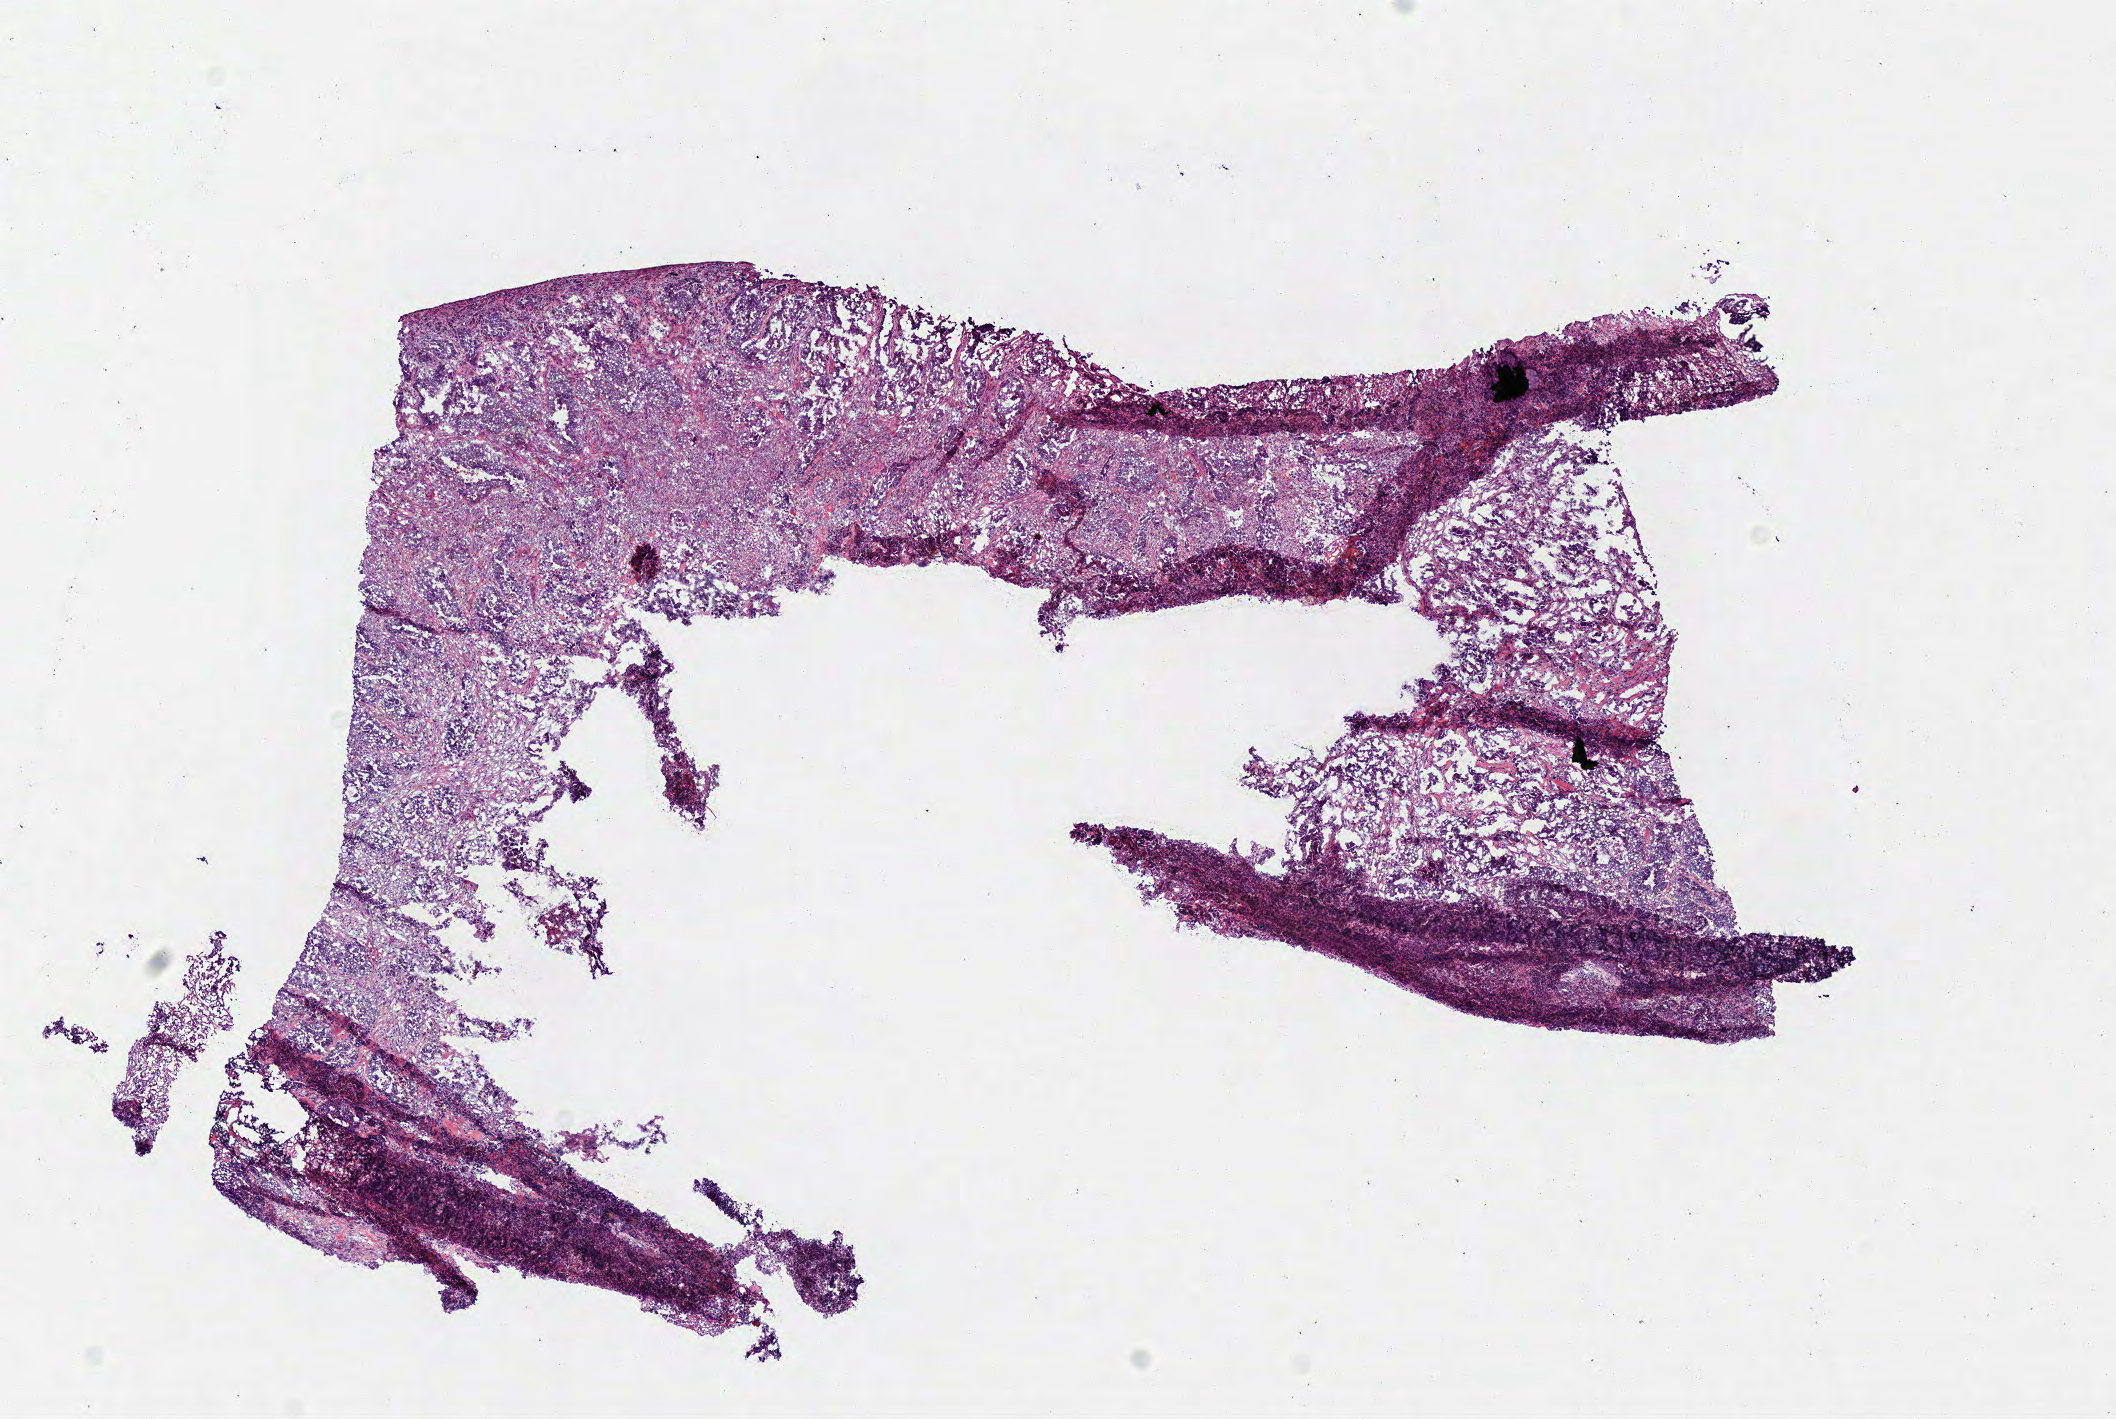
H&E whole-slide image — shown as a low-resolution overview of the whole scanned area (about 8.3 x 5.6 mm, acquisition: 40x scan); frozen section; colon, primary tumour sample. Male patient; age at initial diagnosis 80 years. Pathologist review of this section (percent, as recorded): tumour cells 78%, tumour nuclei 80%, normal cells 2%, stromal cells 15%, necrosis 5%.
AJCC pathologic stage: III (6th edition). Pathologic diagnosis: Adenocarcinoma, NOS (ascending colon).